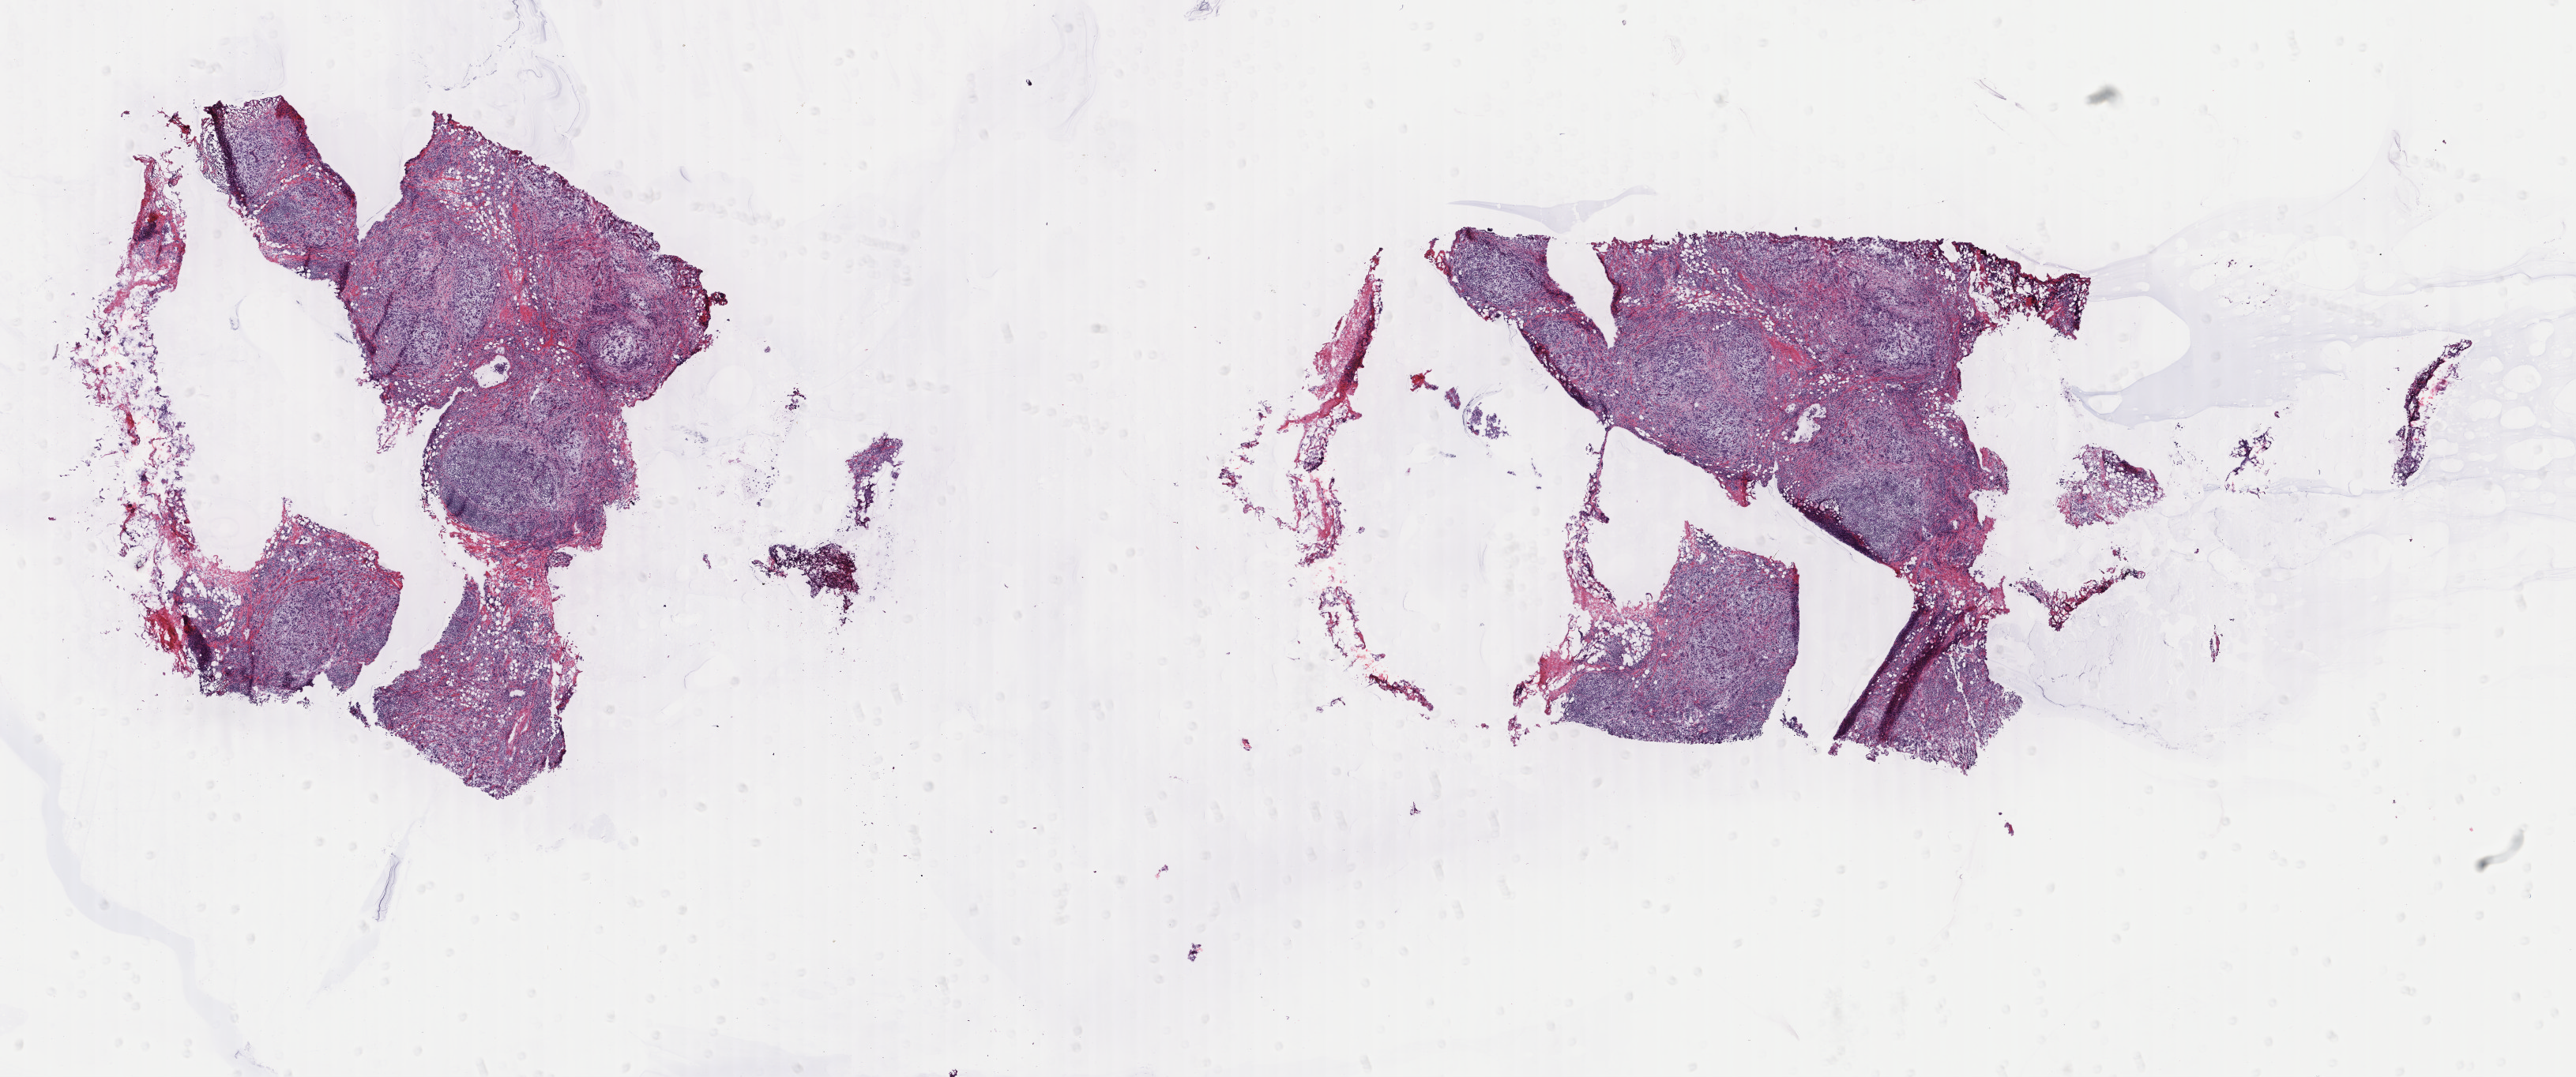
Whole-slide histology image, H&E-stained, whole scanned area (about 25.9 x 10.8 mm, from a 40x scan) shown as a low-resolution overview. Frozen section from the bottom of the tissue portion. Breast, primary tumour sample. Patient: female, age at initial diagnosis 37 years. Composition of this section per pathologist review: tumour cells 40%, tumour nuclei 30%, normal cells 10%, stromal cells 47%, necrosis 3%. Inflammatory infiltration, as recorded: lymphocyte infiltration 60%, monocyte infiltration 1%, neutrophil infiltration 0%.
Laterality: right. Histologic diagnosis: Infiltrating duct carcinoma, NOS. AJCC pathologic stage: IIIA (6th edition). Lymph nodes positive (case pathology): 9 of 14 examined.